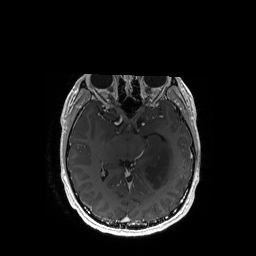
Brain MRI from a brain-tumour surgery series, one axial slice; position 100 of 192 along the scan axis; T1-weighted post-contrast; 1 mm slice thickness; 256 × 256 image matrix, field of view 256 × 256 mm. Case-level facts recorded for this patient, not image findings: histopathology: Astrocytoma; WHO grade: 3; IDH mutation: yes; tumour location: Left Temporal.
Outlined on this slice (manually delineated by an expert):
- tumour: bounding box (x1, y1, x2, y2) in pixels: (145, 144, 172, 189)